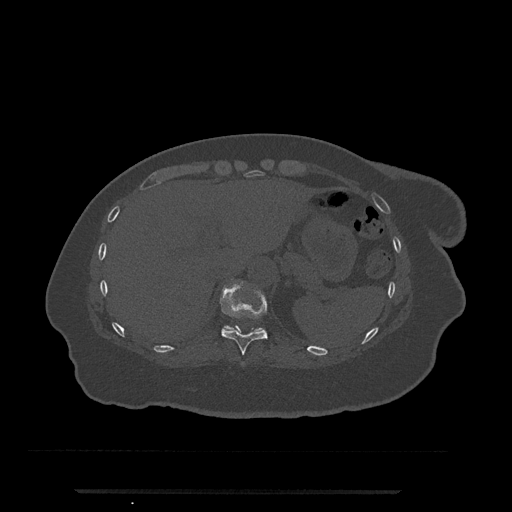
CT including the spine, one axial slice. Slice 272 of 797 in the series (ordered by position). 120 kVp. Bone window (W 1800 / L 400 HU). 512 × 512 image matrix, field of view 440 × 440 mm. Female patient, age 51 years. Case-level facts recorded for this patient, not image findings: primary cancer: neuro; vertebrae with lytic lesions (as recorded): T8.
Annotated regions visible in this slice (semi-automatic segmentation, software-assisted and operator-edited):
- T10 vertebra: bounding box (x1, y1, x2, y2) in pixels: (216, 279, 268, 364)
- T11 vertebra: (225, 326, 261, 331)